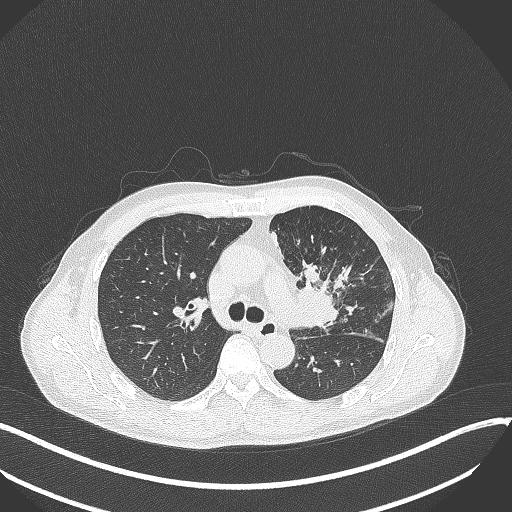
Chest CT, one axial slice. Slice 222 of 411 in the series (ordered by position). Reconstruction kernel B70f. 120 kVp. Lung window (W 1500 / L -600 HU). 1 mm slice thickness. 512 × 512 image matrix, field of view 400 × 400 mm. Male patient, age 56 years. Case-level facts recorded for this patient, not image findings: clinical TNM (as recorded): T2a N0 M0.
Structures marked on this image (bounding box drawn by a radiologist):
- lung tumour (recorded histology: squamous cell carcinoma): bounding box <298,275,337,331> (left, top, right, bottom; pixels)